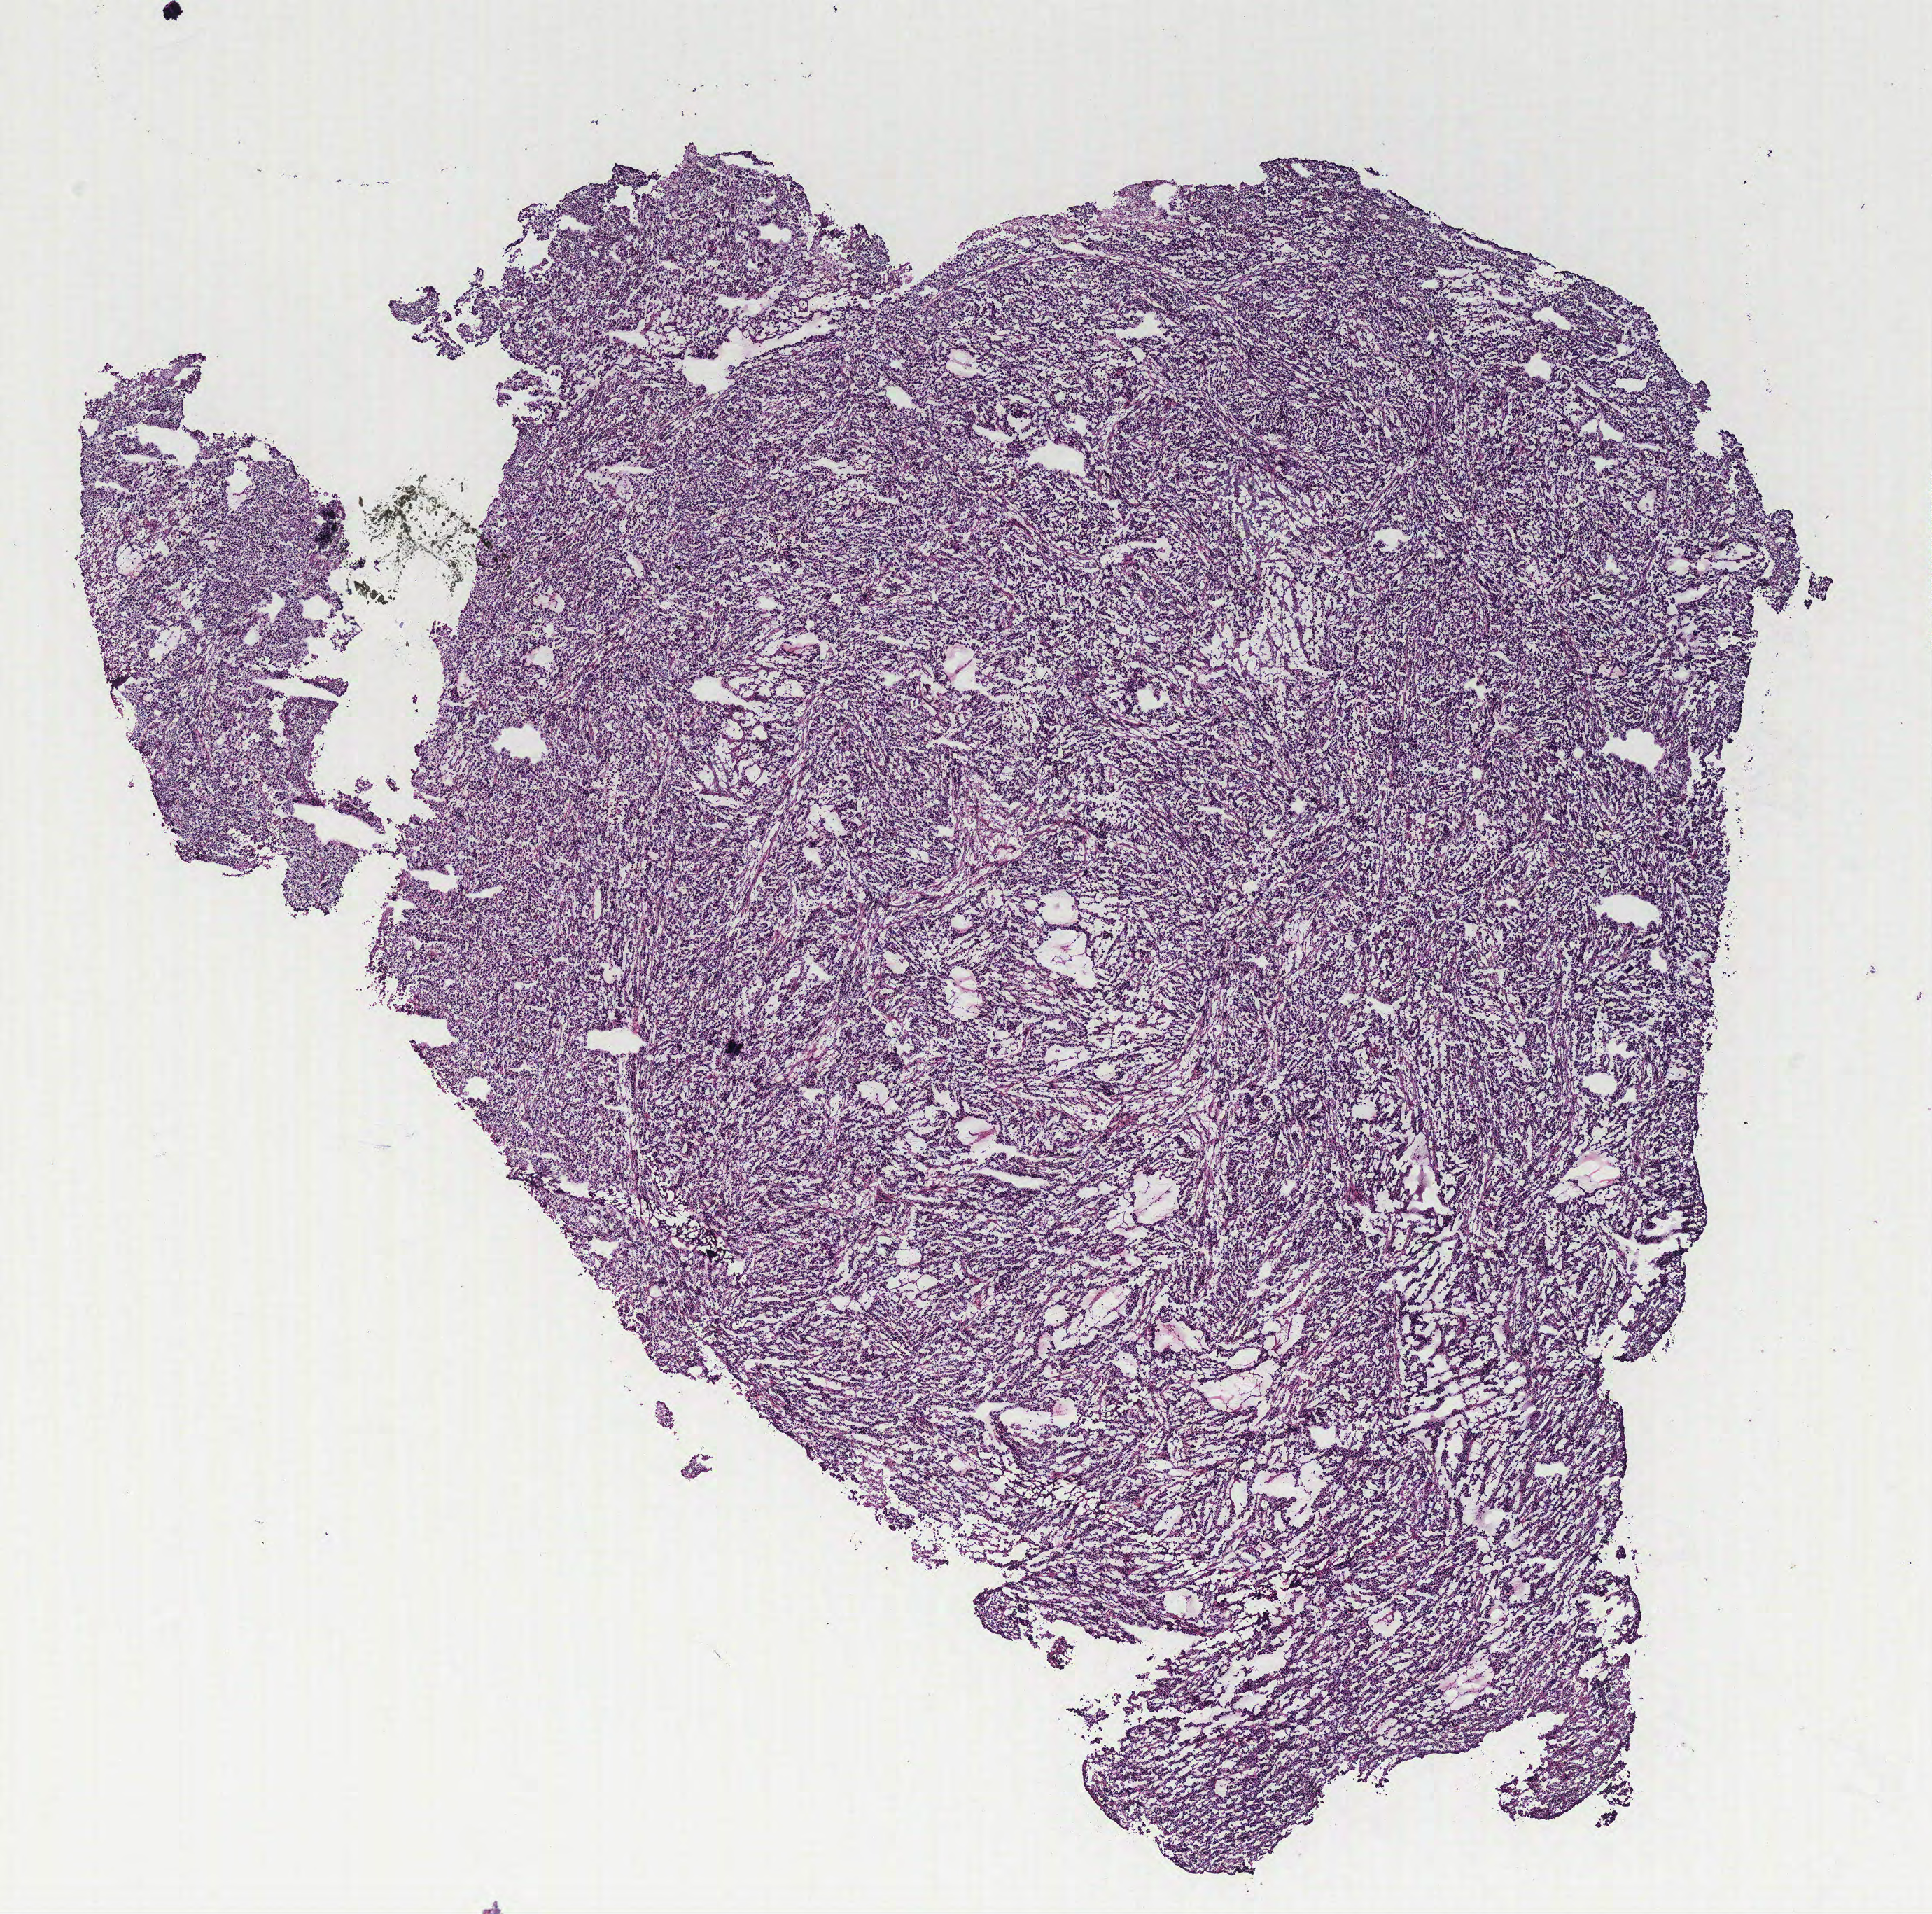
H&E whole-slide image, shown as a low-resolution overview of the whole scanned area (about 11.0 x 10.9 mm, slide scanned at 40x), breast, tissue type not recorded.
Patient diagnosis (cohort enrolment): breast cancer (breast).